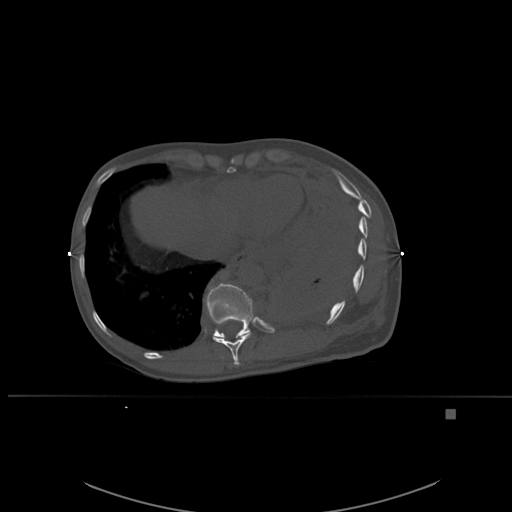
CT including the spine, one axial slice. Bone window (W 1800 / L 400 HU). 512 × 512 image matrix. Patient: female, 45 years. Case-level facts recorded for this patient, not image findings: primary cancer: lung.
Annotated regions visible in this slice (semi-automatic segmentation, software-assisted and operator-edited):
- T10 vertebra: box from (x=213, y=332) to (x=252, y=366) px
- T11 vertebra: (x=206, y=283)–(x=254, y=338)